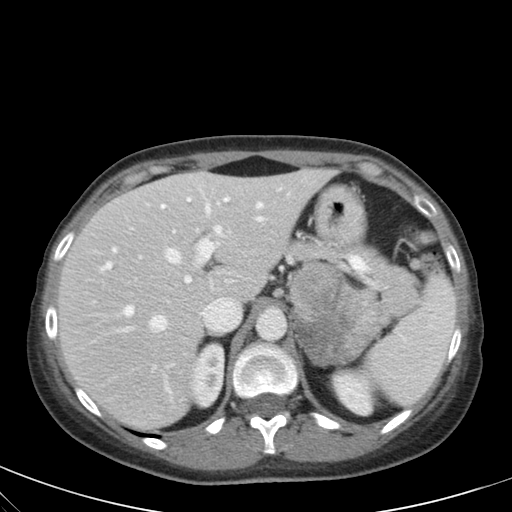
Contrast-enhanced abdominal CT, one axial slice. Slice 42 of 59 in the series (ordered by position). Intravenous contrast given. Soft-tissue window (W 400 / L 40 HU). 4 mm slice thickness. 512 × 512 image matrix, field of view 350 × 350 mm. Female patient, age 28 years. From the clinical record (not read from this slice): diagnosis: adrenocortical carcinoma; tumour side: left adrenal; tumour size at pathology: 7 cm; Ki-67 index: 40 %; stage (as recorded): 4.
Annotated regions visible in this slice (semi-automatic segmentation, software-assisted and operator-edited):
- mass: bounding box [x1, y1, x2, y2] px = [290, 263, 391, 363]